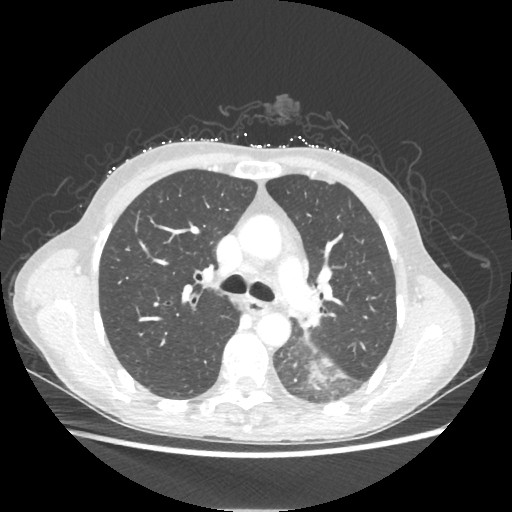
Chest CT, one axial slice. Position 138 of 221 along the scan axis. Reconstruction kernel STANDARD. 80 kVp. Lung window (W 1500 / L -600 HU). 1.25 mm slice thickness. 512 × 512 image matrix, field of view 360 × 360 mm. Female patient, age 53 years. Case-level facts recorded for this patient, not image findings: clinical TNM (as recorded): T3 N0 M0.
Annotated regions visible in this slice (rectangle marked by the reading radiologist):
- lung tumour (recorded histology: adenocarcinoma): bounding box [x1, y1, x2, y2] px = [309, 357, 347, 391]